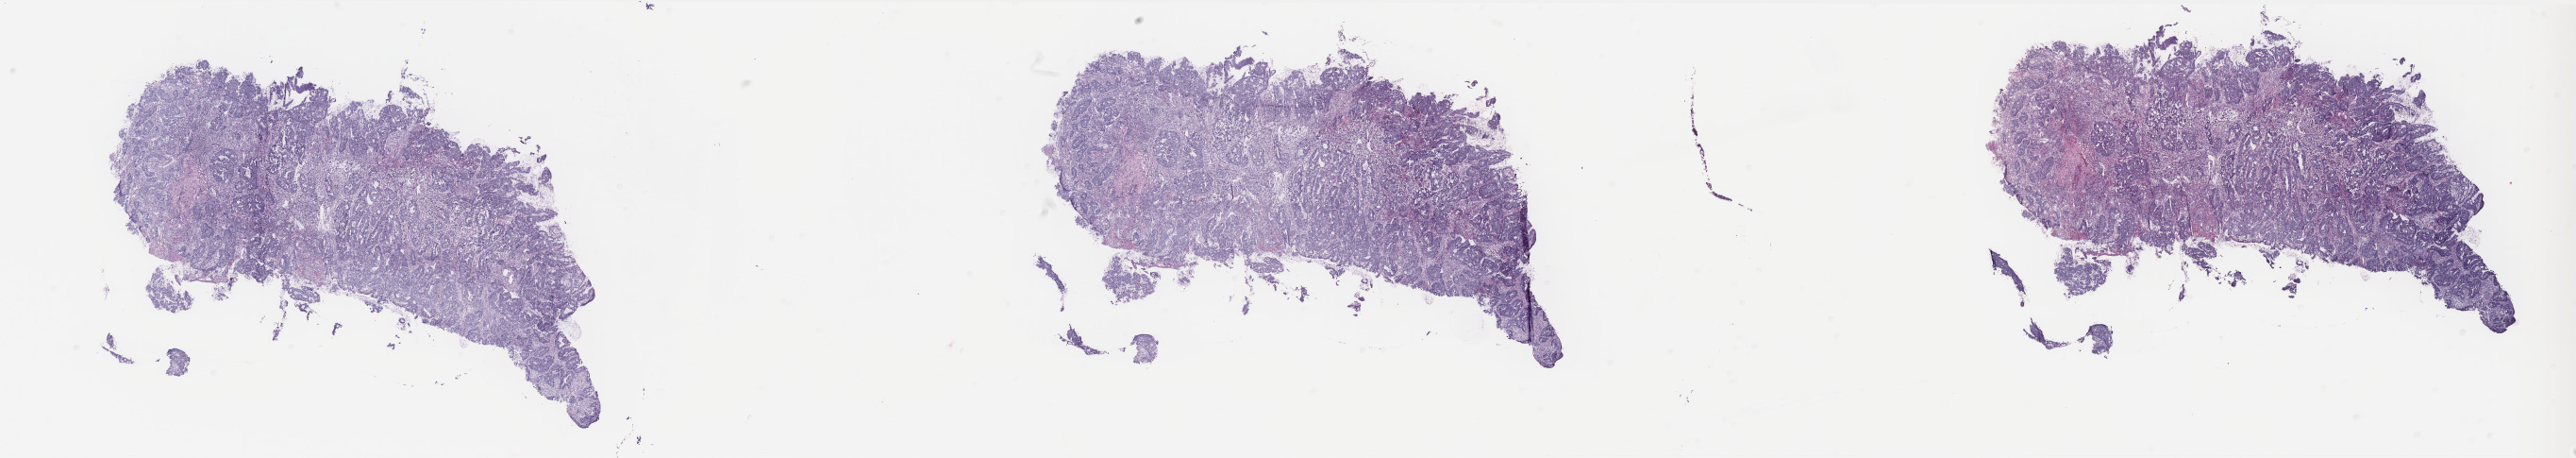
Digitized H&E-stained tissue section (whole slide), low-resolution overview of the scanned area, about 43.8 x 7.8 mm (from a 40x scan). Frozen section from the bottom of the tissue portion. Primary tumour sample from the colon. Male, age 63 years at initial diagnosis. Slide review estimates, as recorded: tumour cells 55%, tumour nuclei 70%, normal cells 5%, stromal cells 37%, necrosis 3%. Inflammatory infiltration, as recorded: lymphocyte infiltration 12%, monocyte infiltration 0%, neutrophil infiltration 6%.
TNM: T3 N0 M0. AJCC pathologic stage: IIA. Histologic diagnosis: Mucinous adenocarcinoma (cecum). Lymph nodes positive (case pathology): 0 of 22 examined.